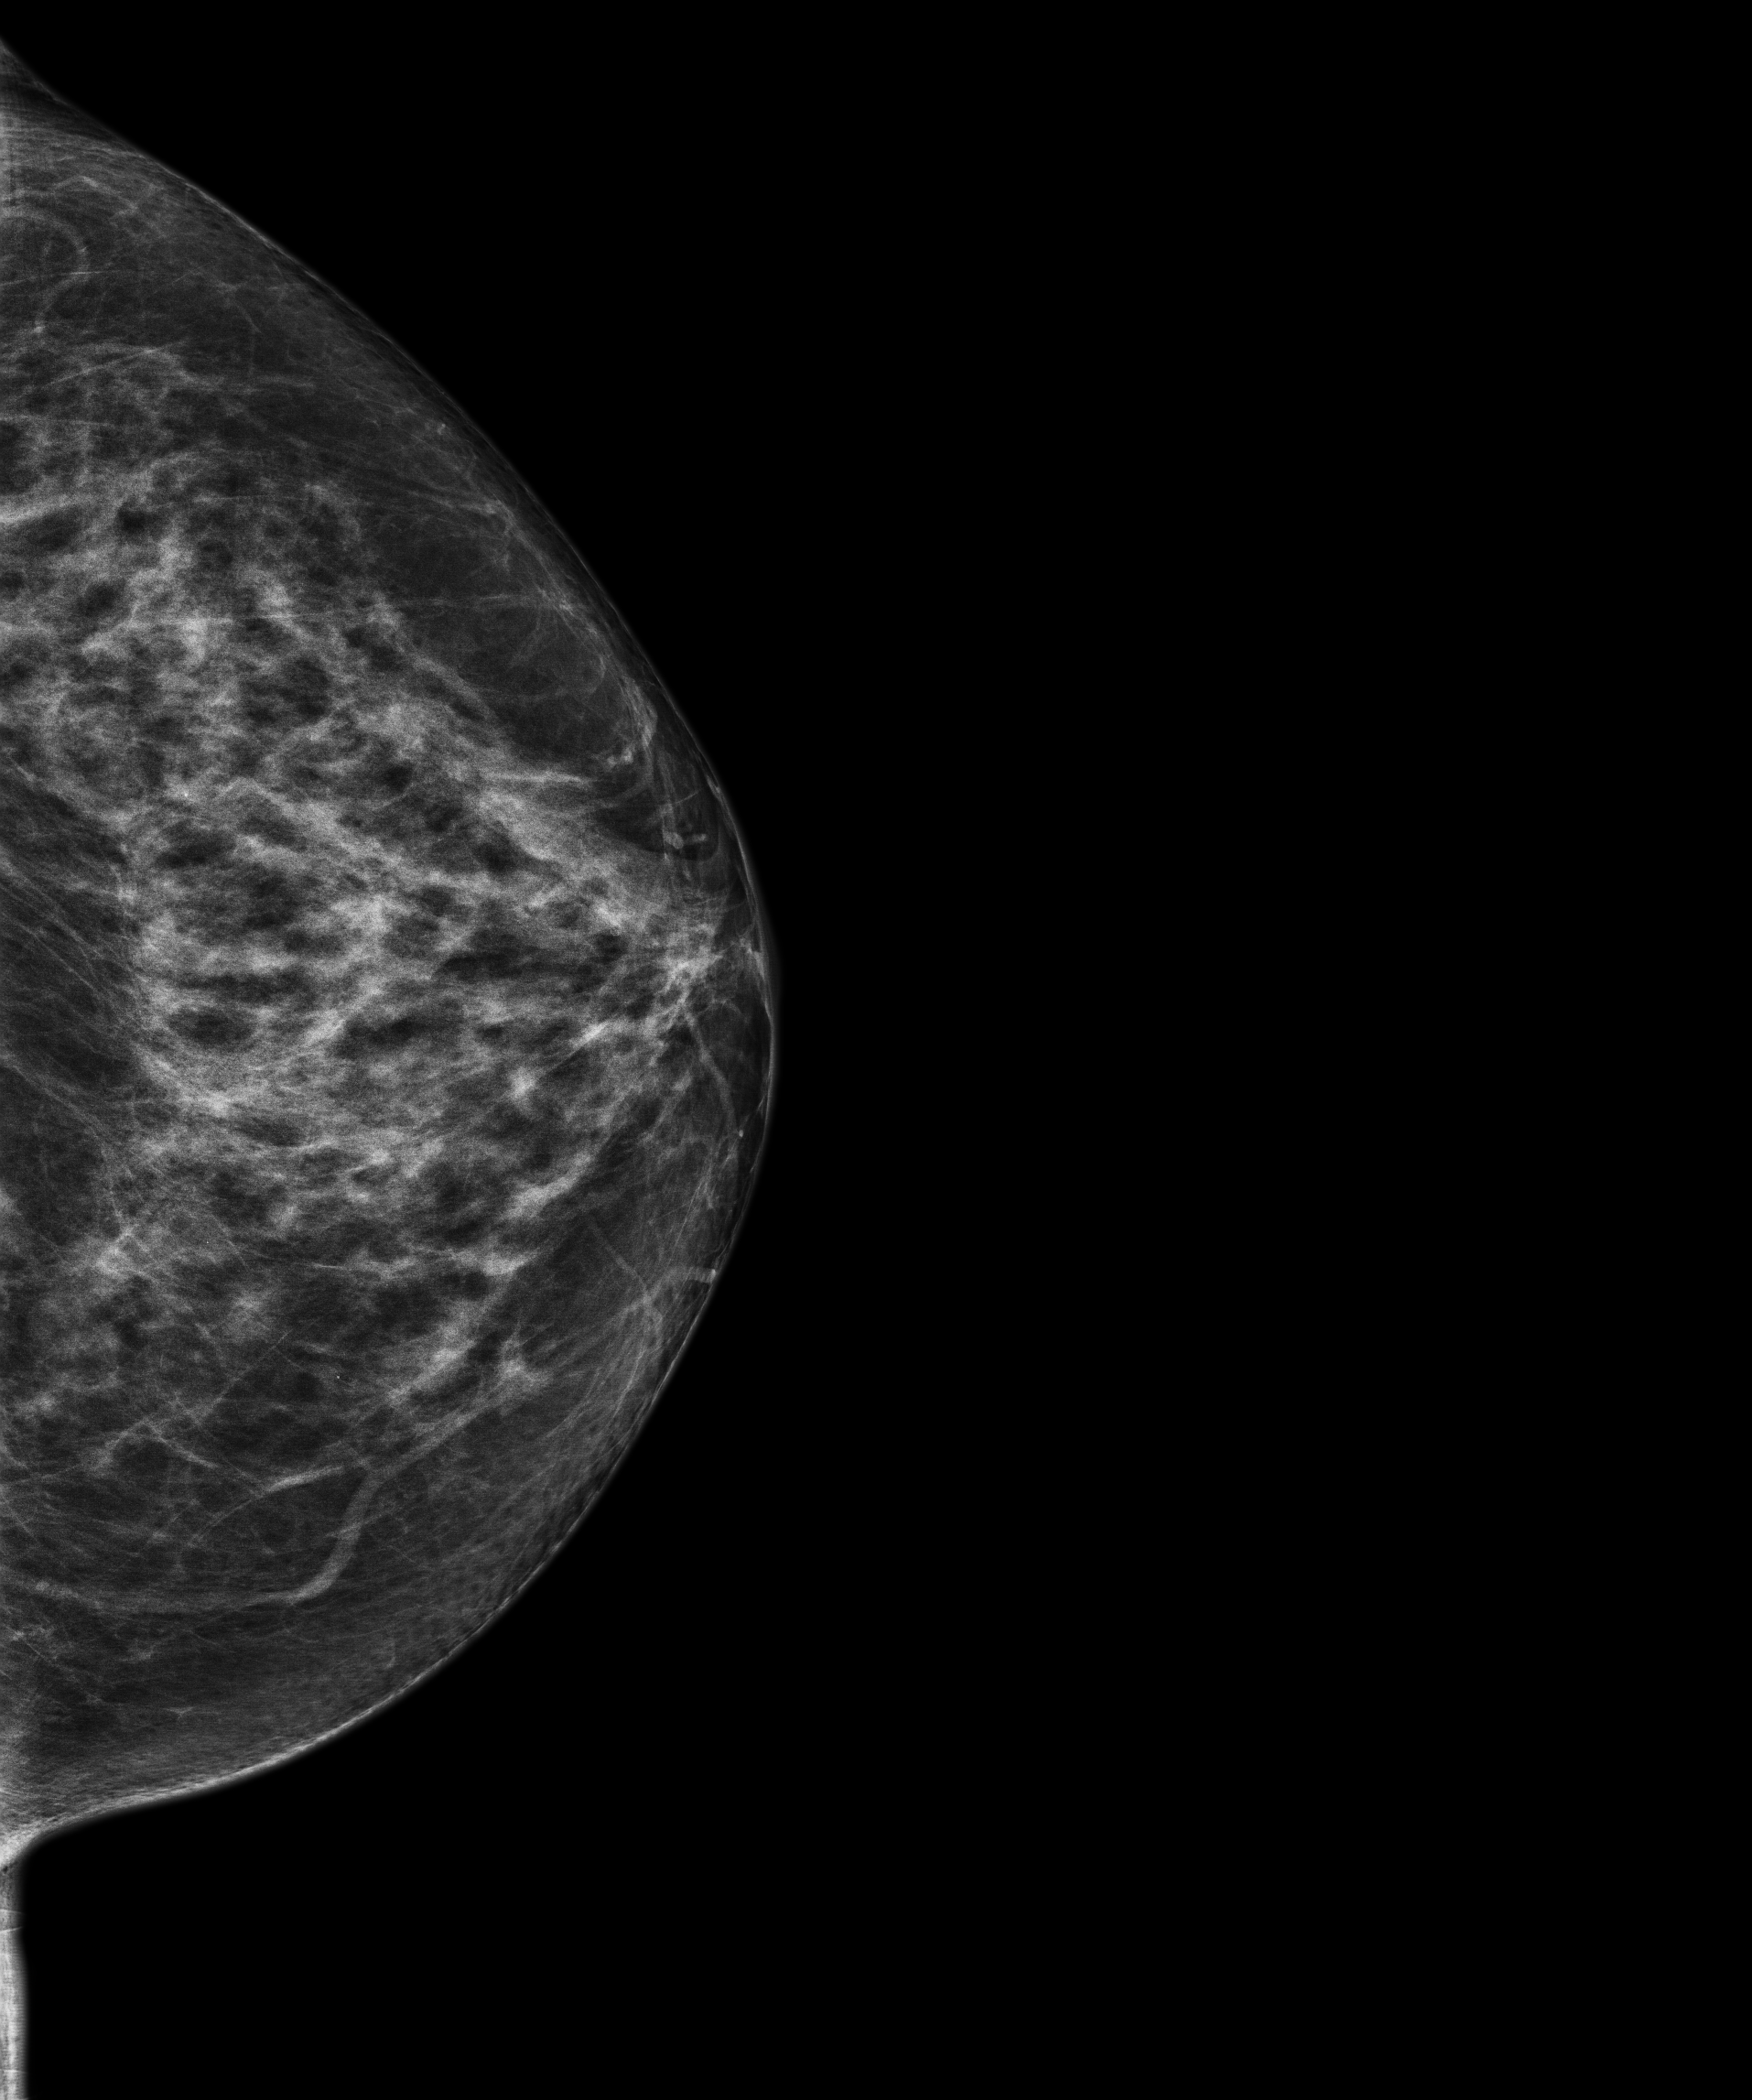
Annual screening mammography examination, system: Senographe Pristina. Patient: female, 59 years.
Image type: full-field digital mammogram. Breast: left. Projection: craniocaudal (CC) view.